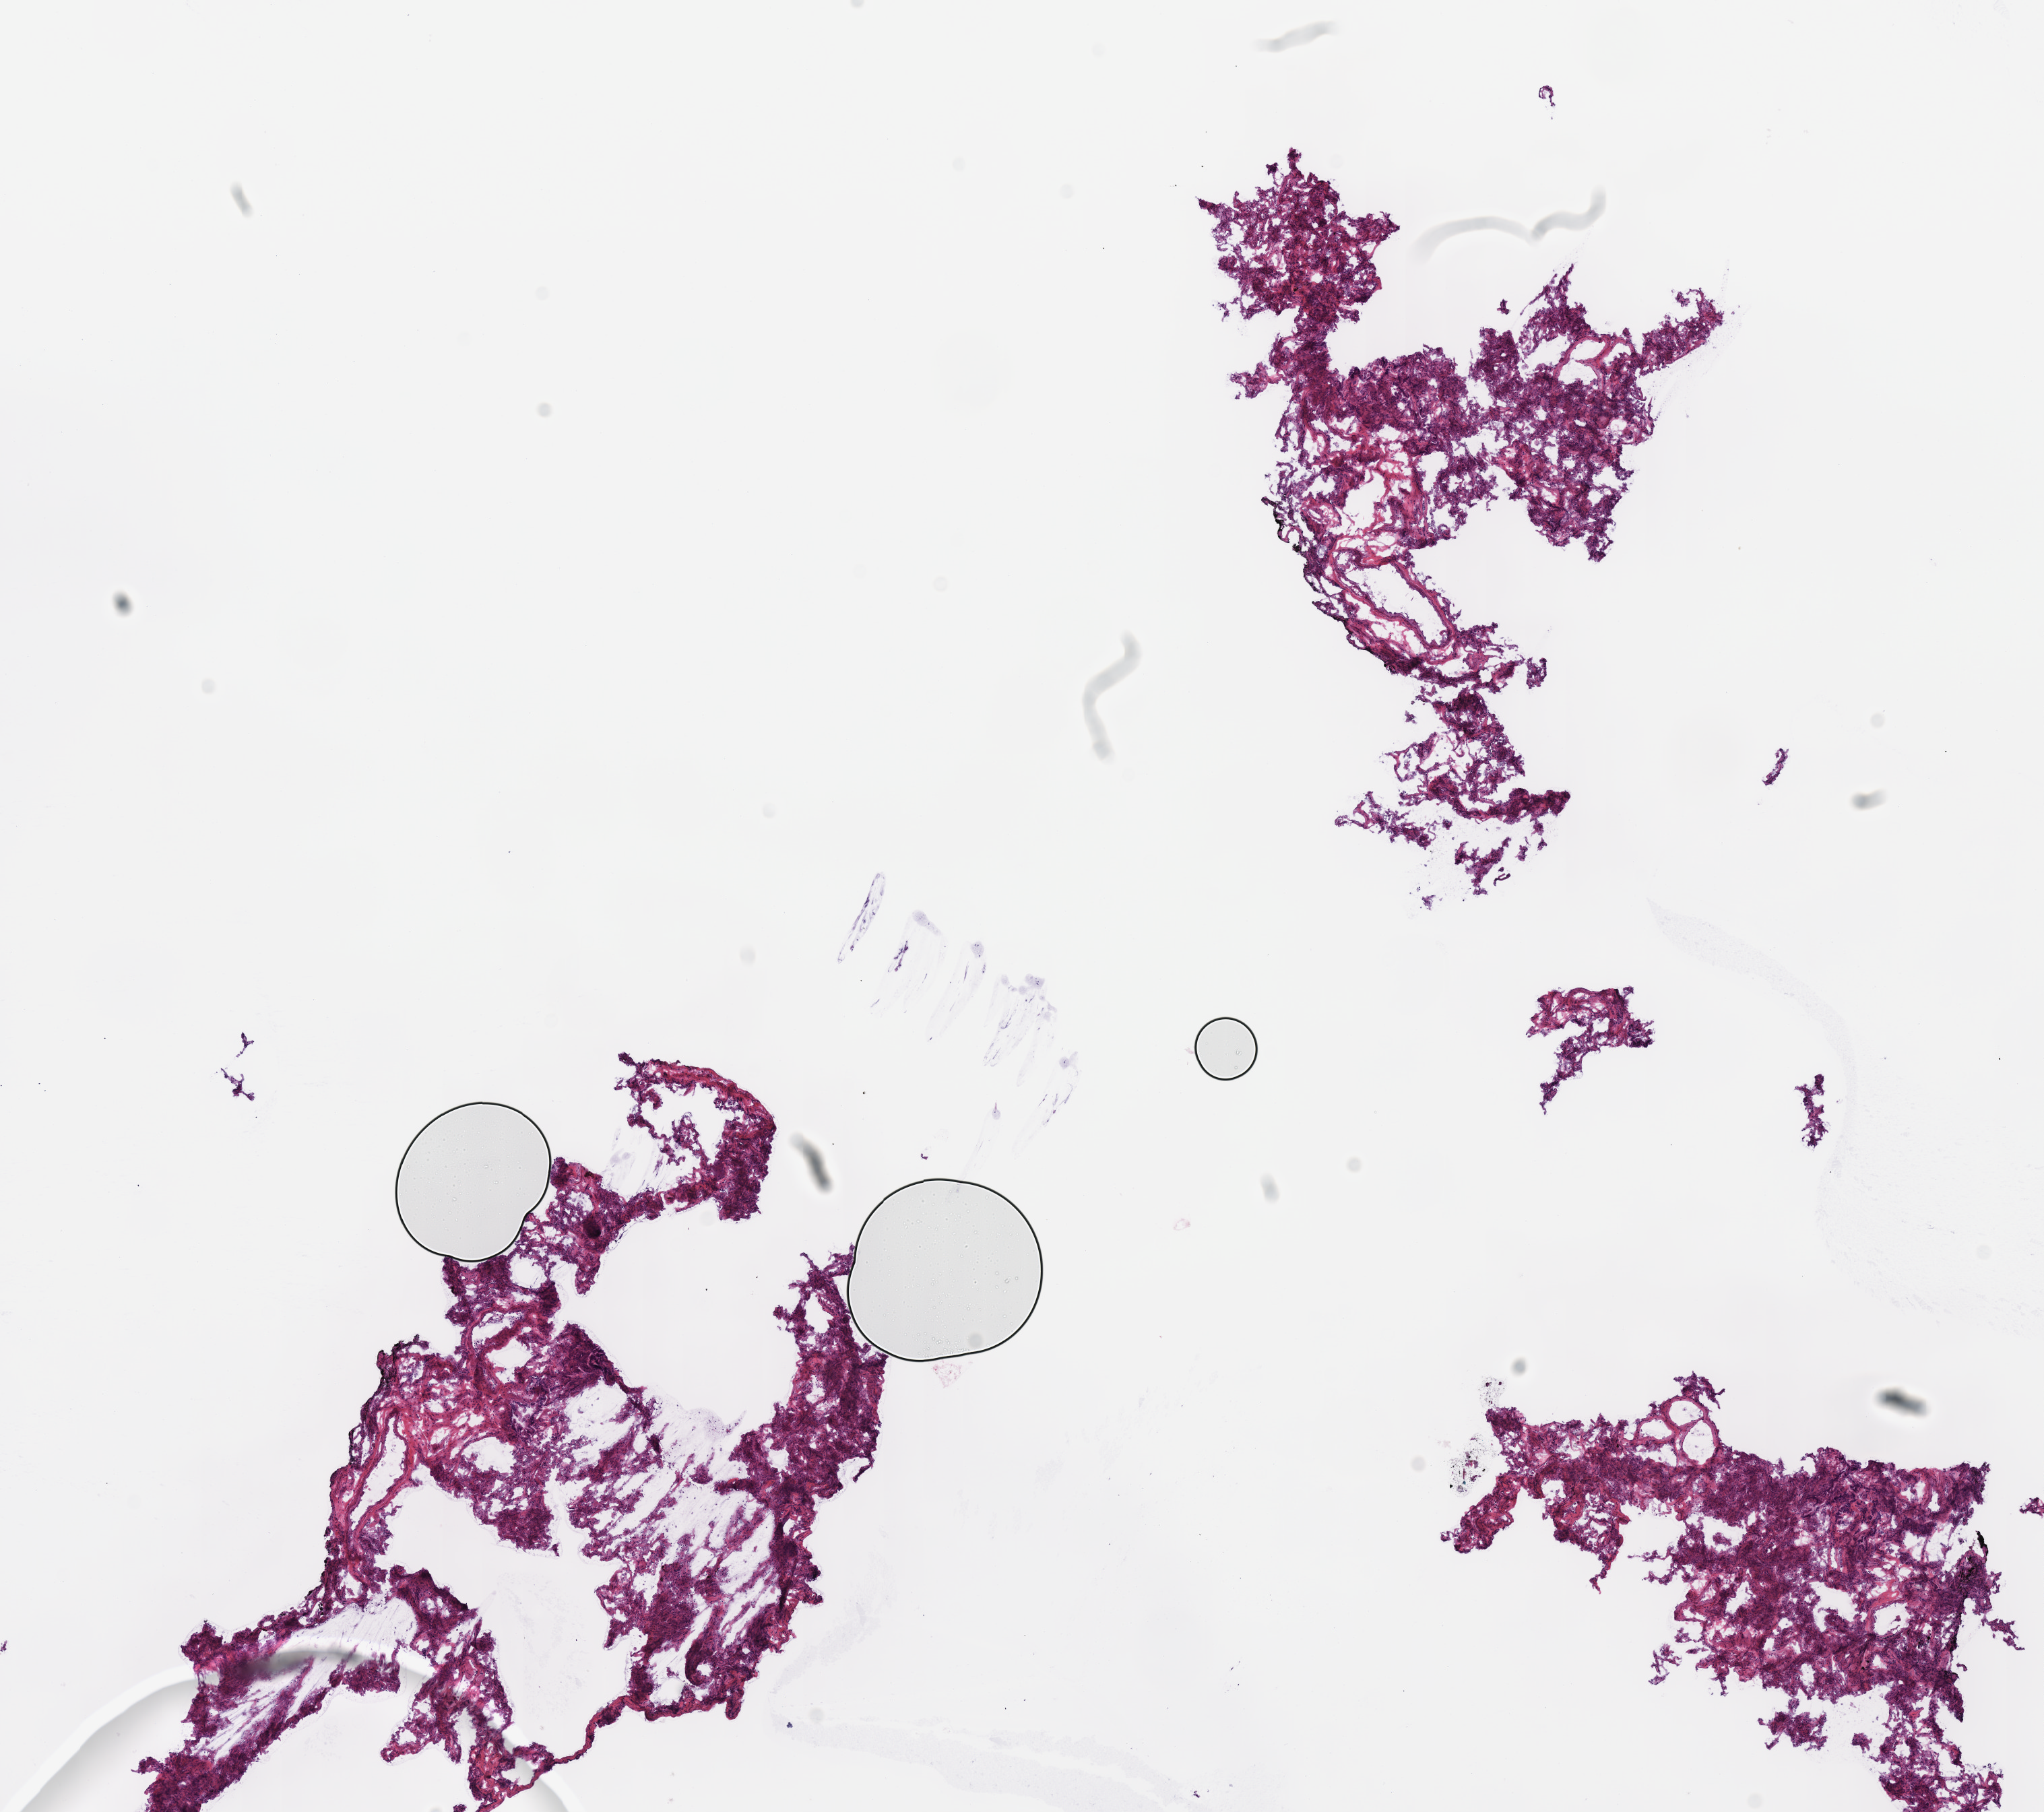
Hematoxylin and eosin (H&E) stained whole-slide image, low-resolution overview of the scanned area, about 12.0 x 10.6 mm (from a 40x scan); frozen section; lung, solid tissue normal (non-tumour tissue) sample. Male, age 76 years at initial diagnosis.
This section: solid tissue normal (non-tumour) sample from the same patient. Patient diagnosis: Adenocarcinoma, NOS.